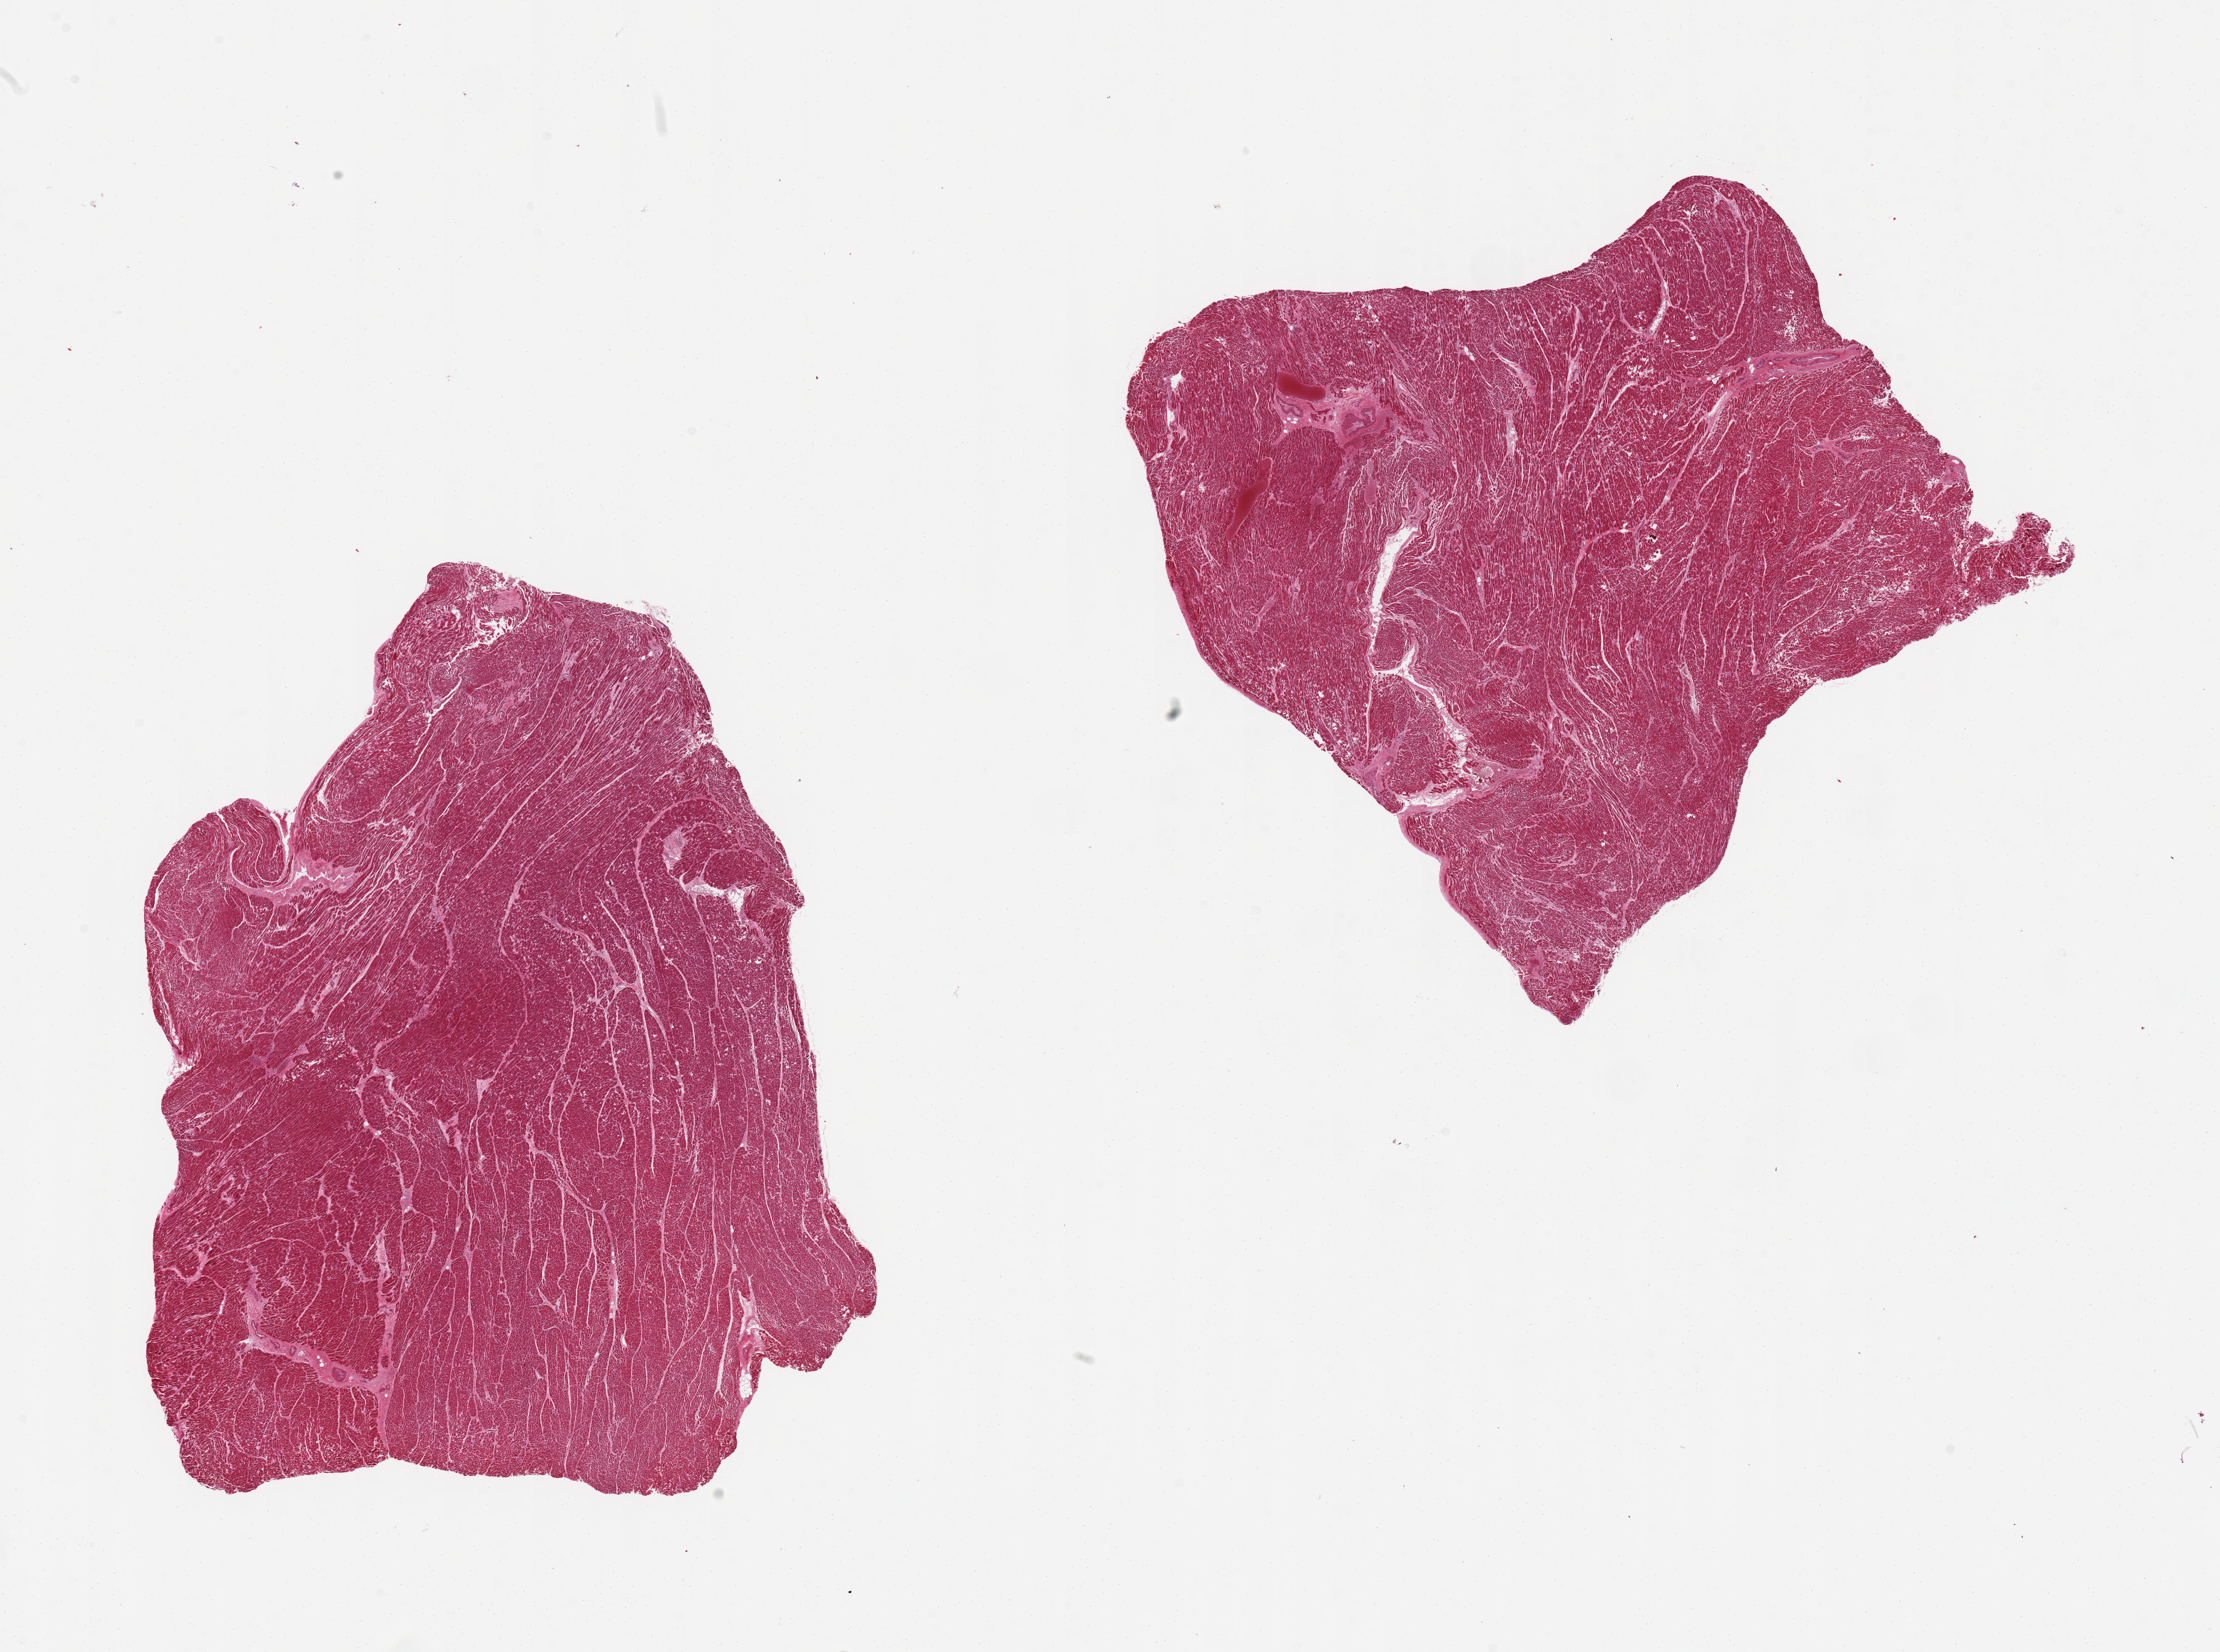
Digitized hematoxylin and eosin (H&E)-stained section, brightfield — a low-resolution overview of the entire scanned area, about 24.6 x 18.3 mm (from a 20x scan), PAXgene-fixed paraffin-embedded (PFPE) section, target tissue: heart, donor tissue sample. Donor: male.
* pathologist's review note for this sample: 2 pieces; hypertrophied fibers